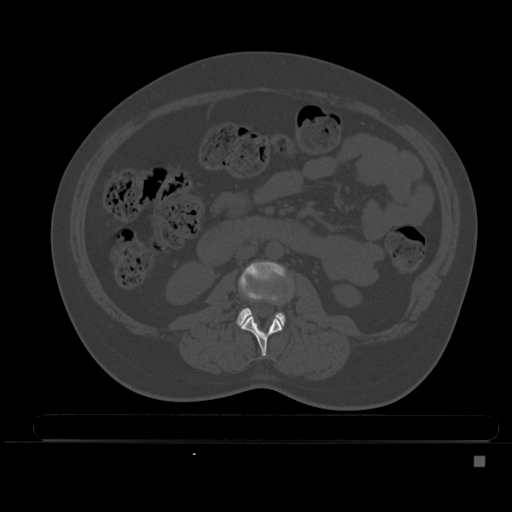
CT including the spine, one axial slice; slice 162 of 495 in the series (ordered by position); bone window (W 1800 / L 400 HU); 1.5 mm slice thickness; 512 × 512 image matrix, field of view 404 × 404 mm. Female patient, age 33 years. Case-level facts recorded for this patient, not image findings: primary cancer: breast; vertebrae with lytic lesions (as recorded): T1.
Outlined on this slice (semi-automatically segmented with operator editing):
- L2 vertebra: bounding box (x1, y1, x2, y2) in pixels: (239, 315, 283, 357)
- L3 vertebra: (237, 261, 286, 326)